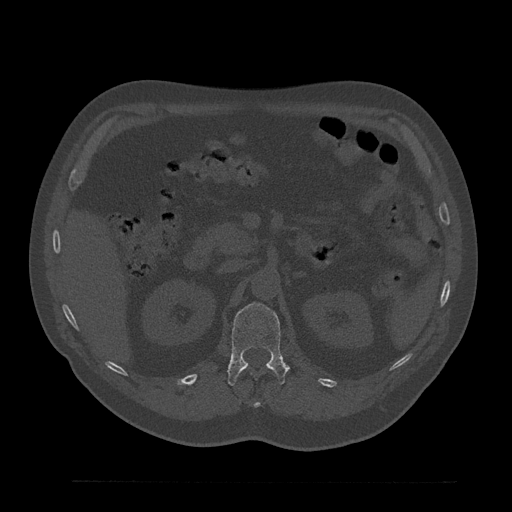
CT including the spine, one axial slice; slice 182 of 797 in the series (ordered by position); bone window (W 1800 / L 400 HU); 512 × 512 image matrix, field of view 430 × 430 mm. Patient: male, 61 years. Case-level facts recorded for this patient, not image findings: primary cancer: prostate.
Annotated regions visible in this slice (semi-automatic segmentation, software-assisted and operator-edited):
- L1 vertebra: bounding box <228,303,289,386> (left, top, right, bottom; pixels)
- T12 vertebra: <254,403,261,408>